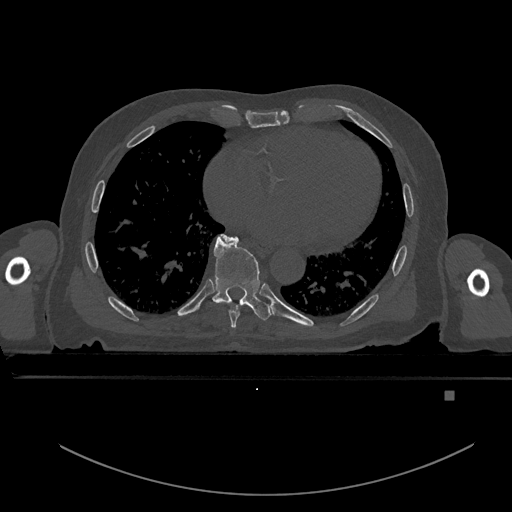
CT including the spine, one axial slice. Slice 219 of 969 in the series (ordered by position). Bone window (W 1800 / L 400 HU). 512 × 512 image matrix, field of view 456 × 456 mm. Male patient, age 82 years. Case-level facts recorded for this patient, not image findings: primary cancer: prostate; vertebrae with lytic lesions (as recorded): T11, T9, T8, T2.
Outlined on this slice (semi-automatically segmented with operator editing):
- T7 vertebra: bounding box (x1, y1, x2, y2) in pixels: (223, 235, 240, 327)
- T8 vertebra: (213, 235, 273, 320)